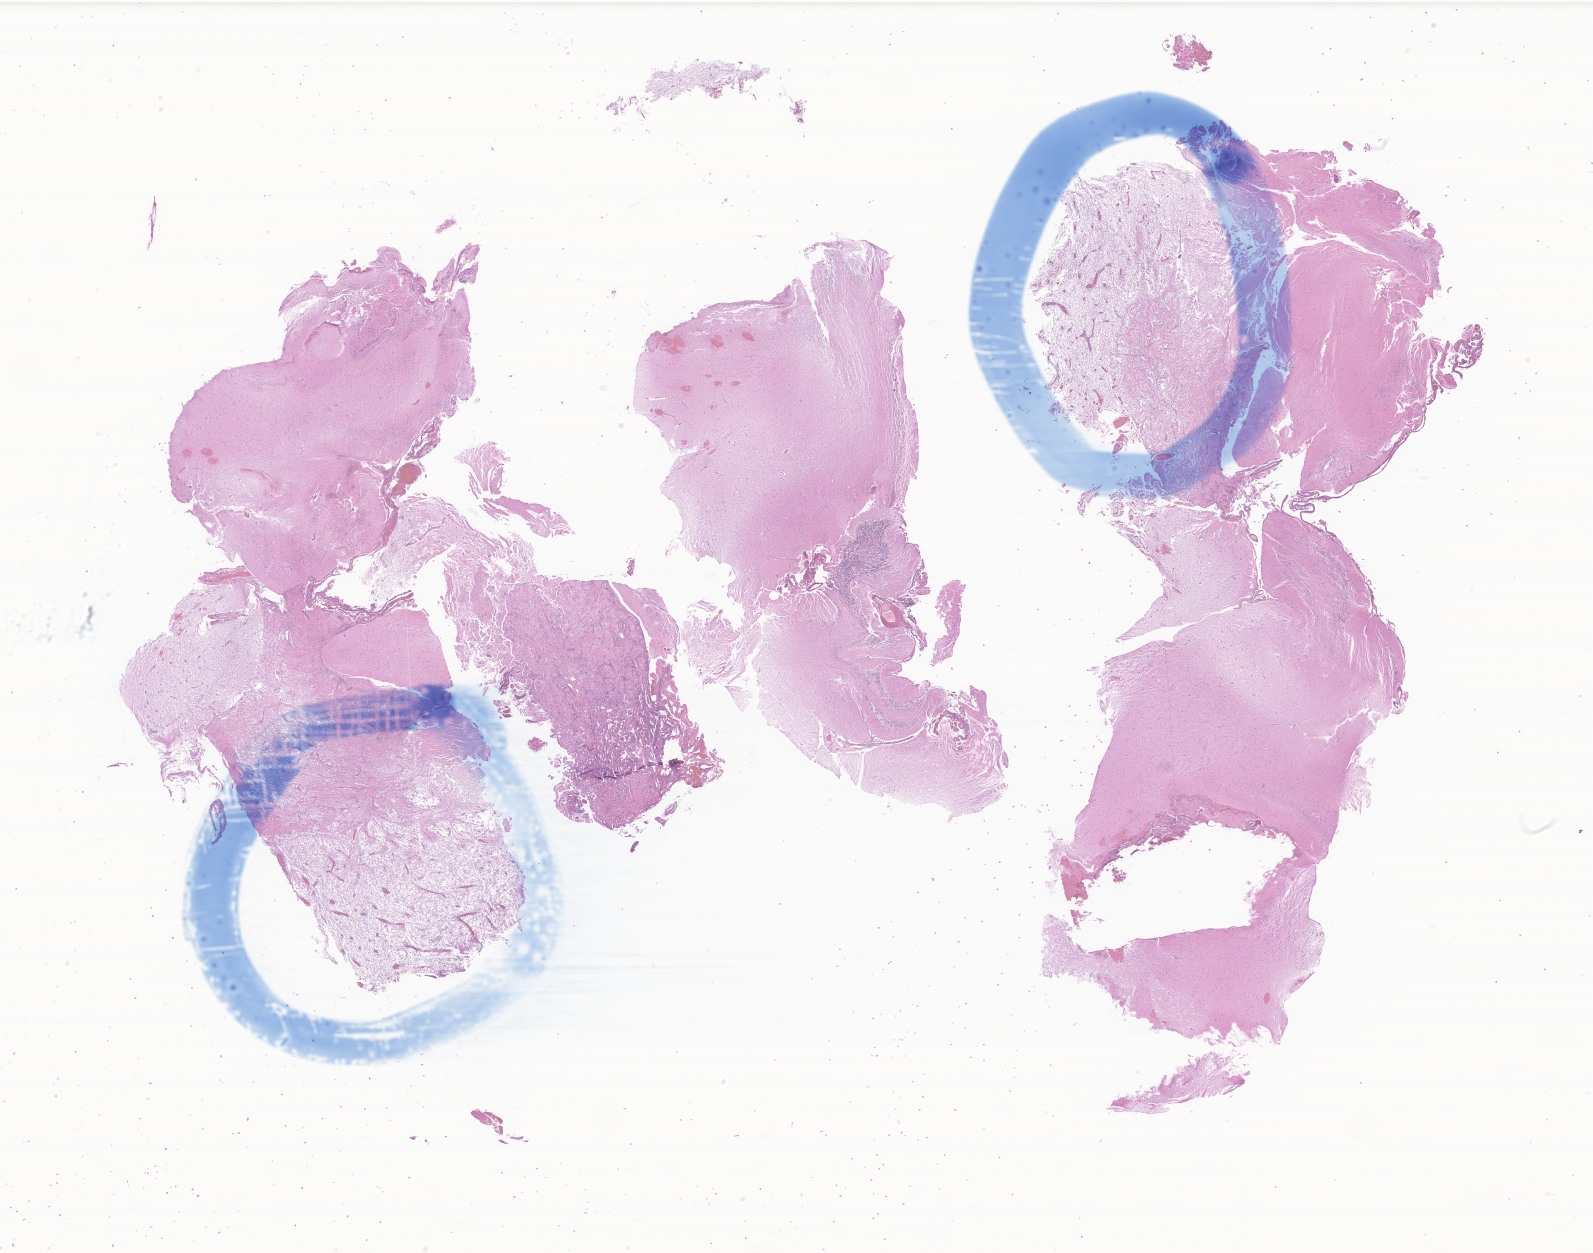
Digitized hematoxylin and eosin (H&E)-stained section of tumor tissue from the brain, whole scanned area (about 26.9 x 21.1 mm) shown as a low-resolution overview. Formalin-fixed, paraffin-embedded (FFPE) tissue. Patient: female, age 64 months (5 years 4 months).
Recorded diagnosis: Pilocytic astrocytoma.